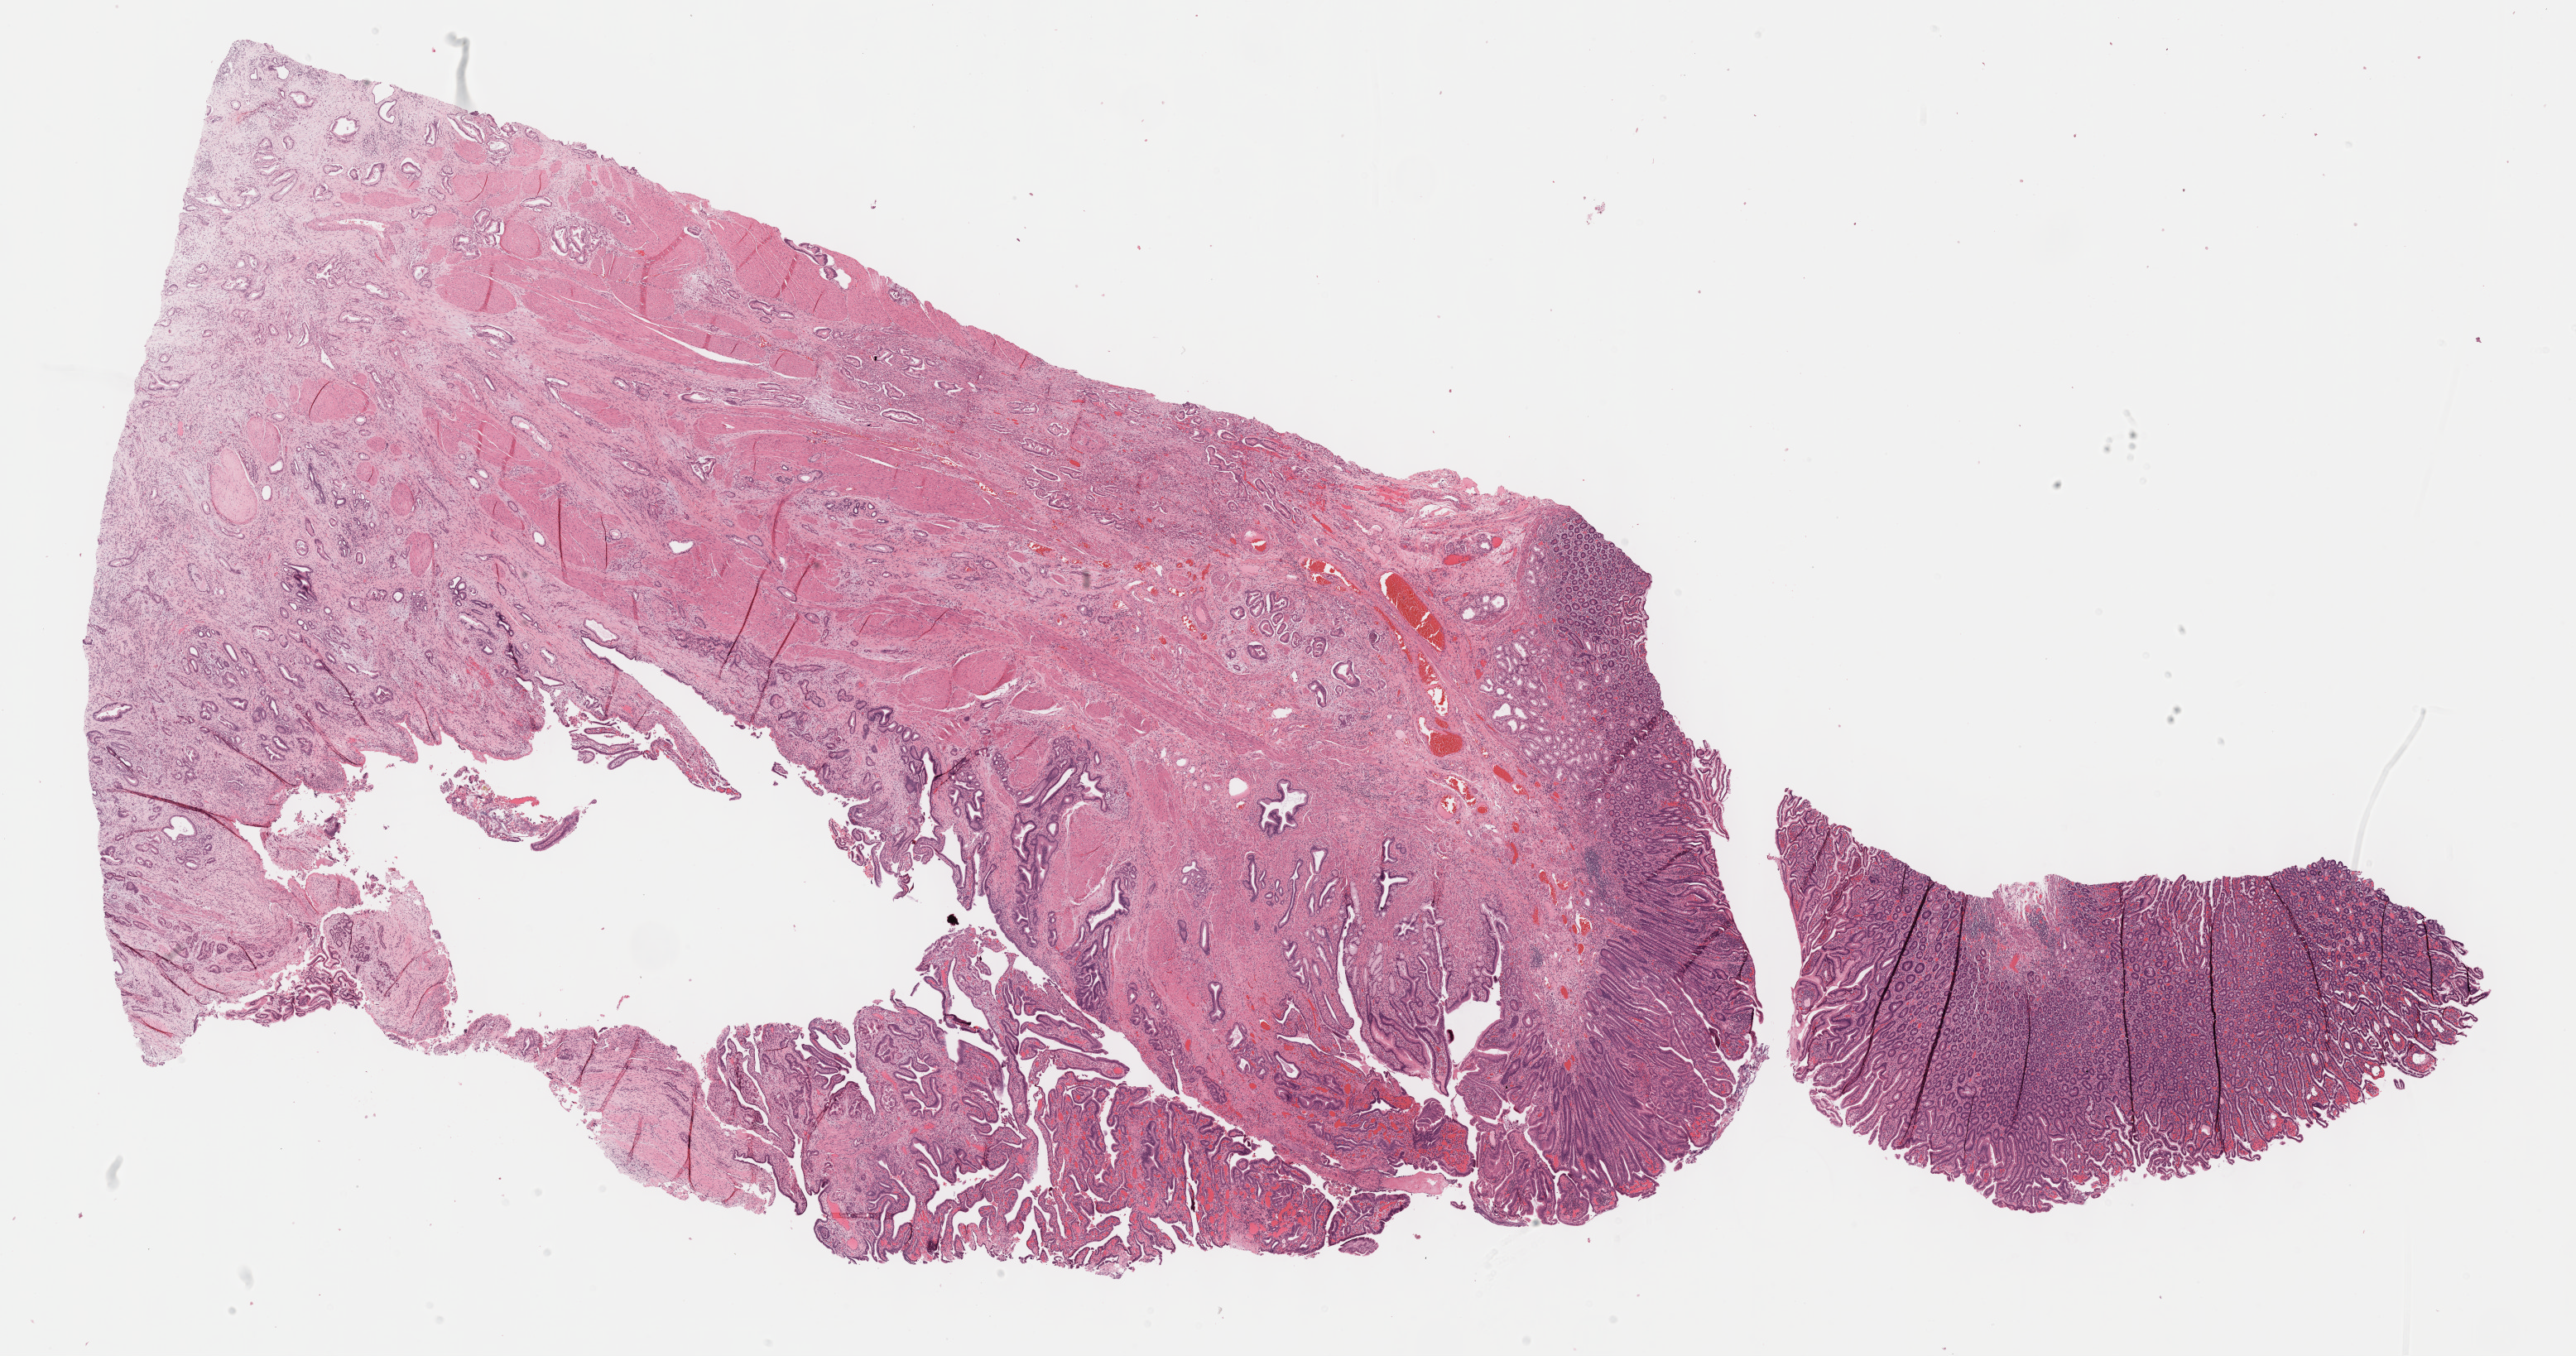
H&E whole-slide image, whole scanned area (about 25.2 x 13.2 mm) shown as a low-resolution overview; formalin-fixed paraffin-embedded (FFPE) diagnostic section; sample: primary tumour, pancreas. Male patient; age at initial diagnosis 80 years. Histologic grade: G2 (moderately differentiated).
Diagnosis: Infiltrating duct carcinoma, NOS (head of pancreas). Lymph nodes positive (case pathology): 2 of 3 examined. AJCC pathologic stage: IIB.